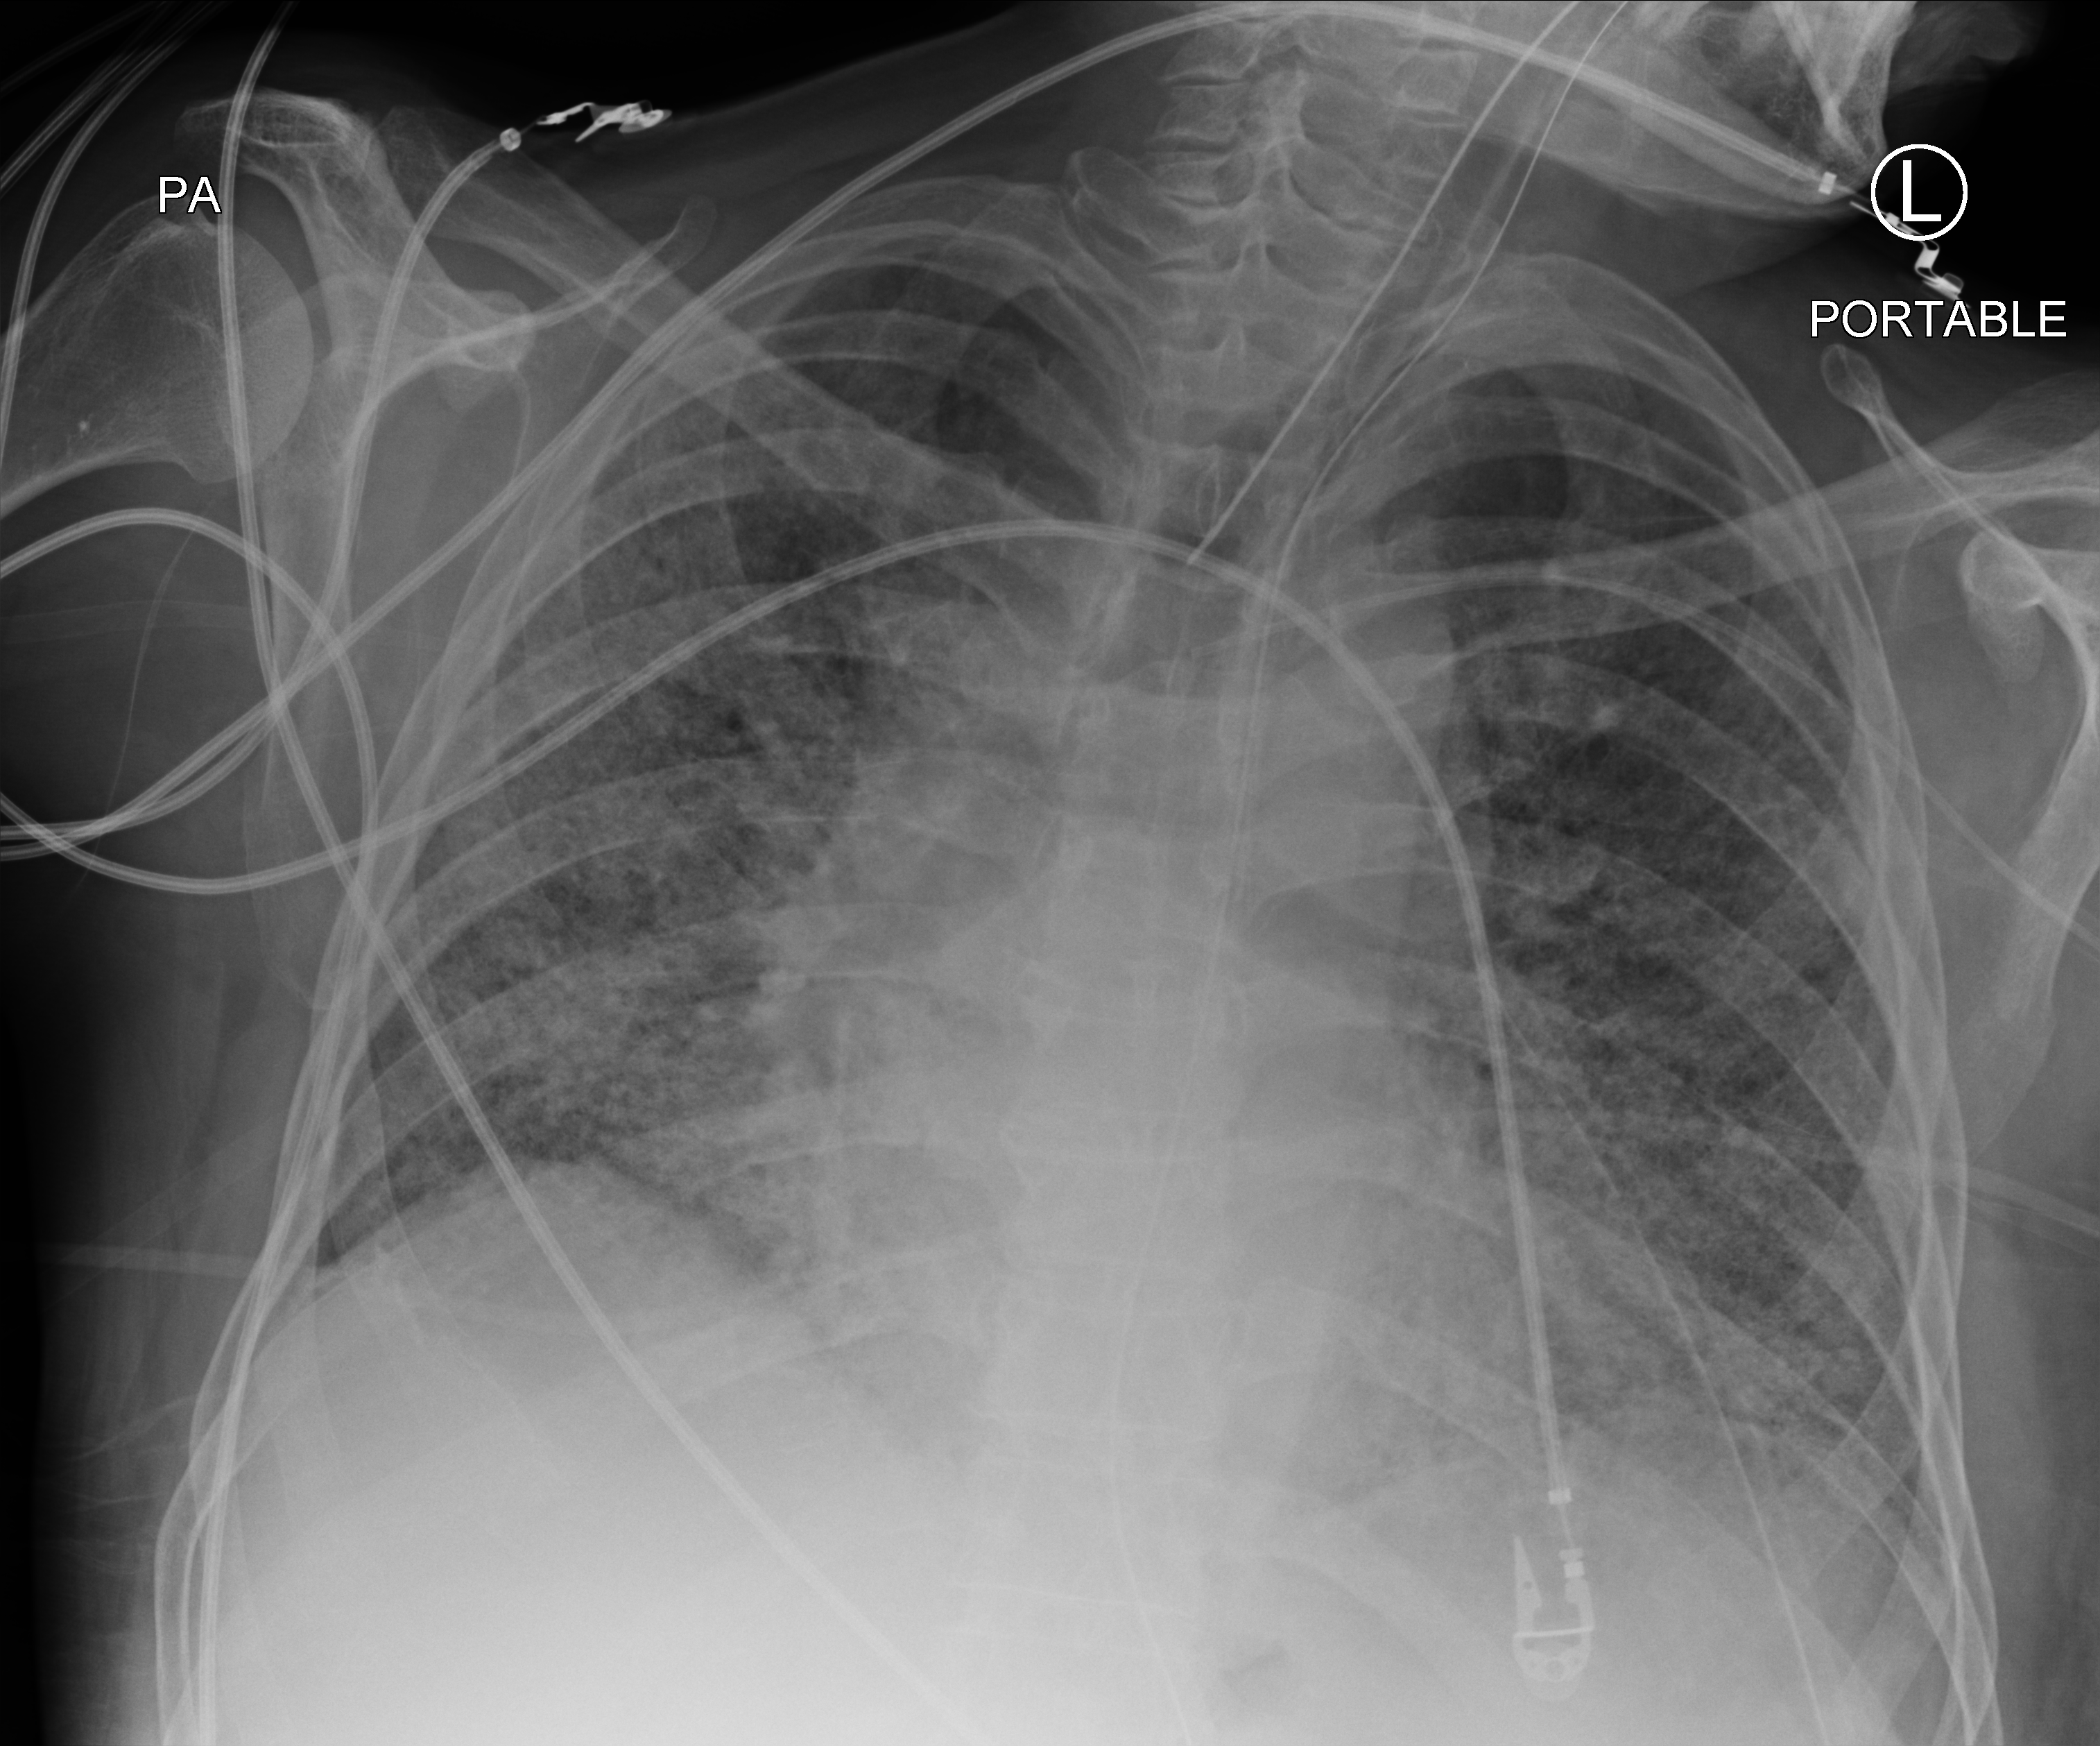
Chest X-ray (portable), posteroanterior (PA) projection. Patient hospitalised with COVID-19; male, aged 60–74 years.
From the hospital-stay record, not from the radiograph (when in the stay this image was taken is not recorded): mechanically ventilated during this hospital stay: yes; admitted to intensive care during this hospital stay: yes.